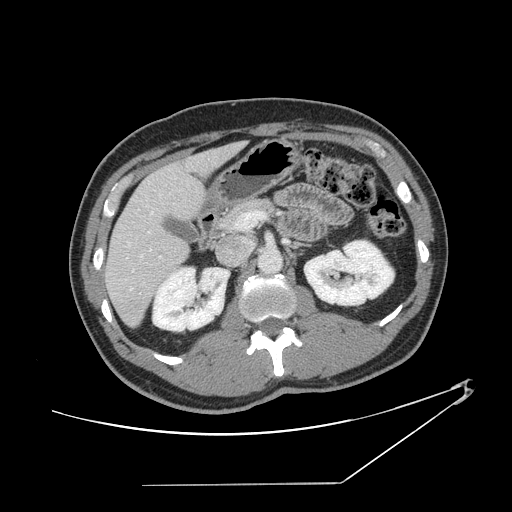
Contrast-enhanced abdominal CT, one axial slice. Slice 71 of 152 in the series (ordered by position). Intravenous contrast given. Soft-tissue window (W 400 / L 40 HU). 2.5 mm slice thickness. 512 × 512 image matrix. Male patient, age 45 years. Case-level facts recorded for this patient, not image findings: diagnosis: colorectal cancer liver metastases, imaged before liver resection; multiple liver metastases: no; largest metastasis: 1 cm; disease in both lobes: no.
Annotated regions visible in this slice (expert manual segmentation):
- hepatic veins: bounding box [x1, y1, x2, y2] px = [125, 194, 161, 290]
- liver: [106, 144, 241, 326]
- planned liver remnant (the part of the liver to remain after resection): [106, 161, 203, 326]
- portal vein (with intrahepatic branches): [235, 211, 265, 229]